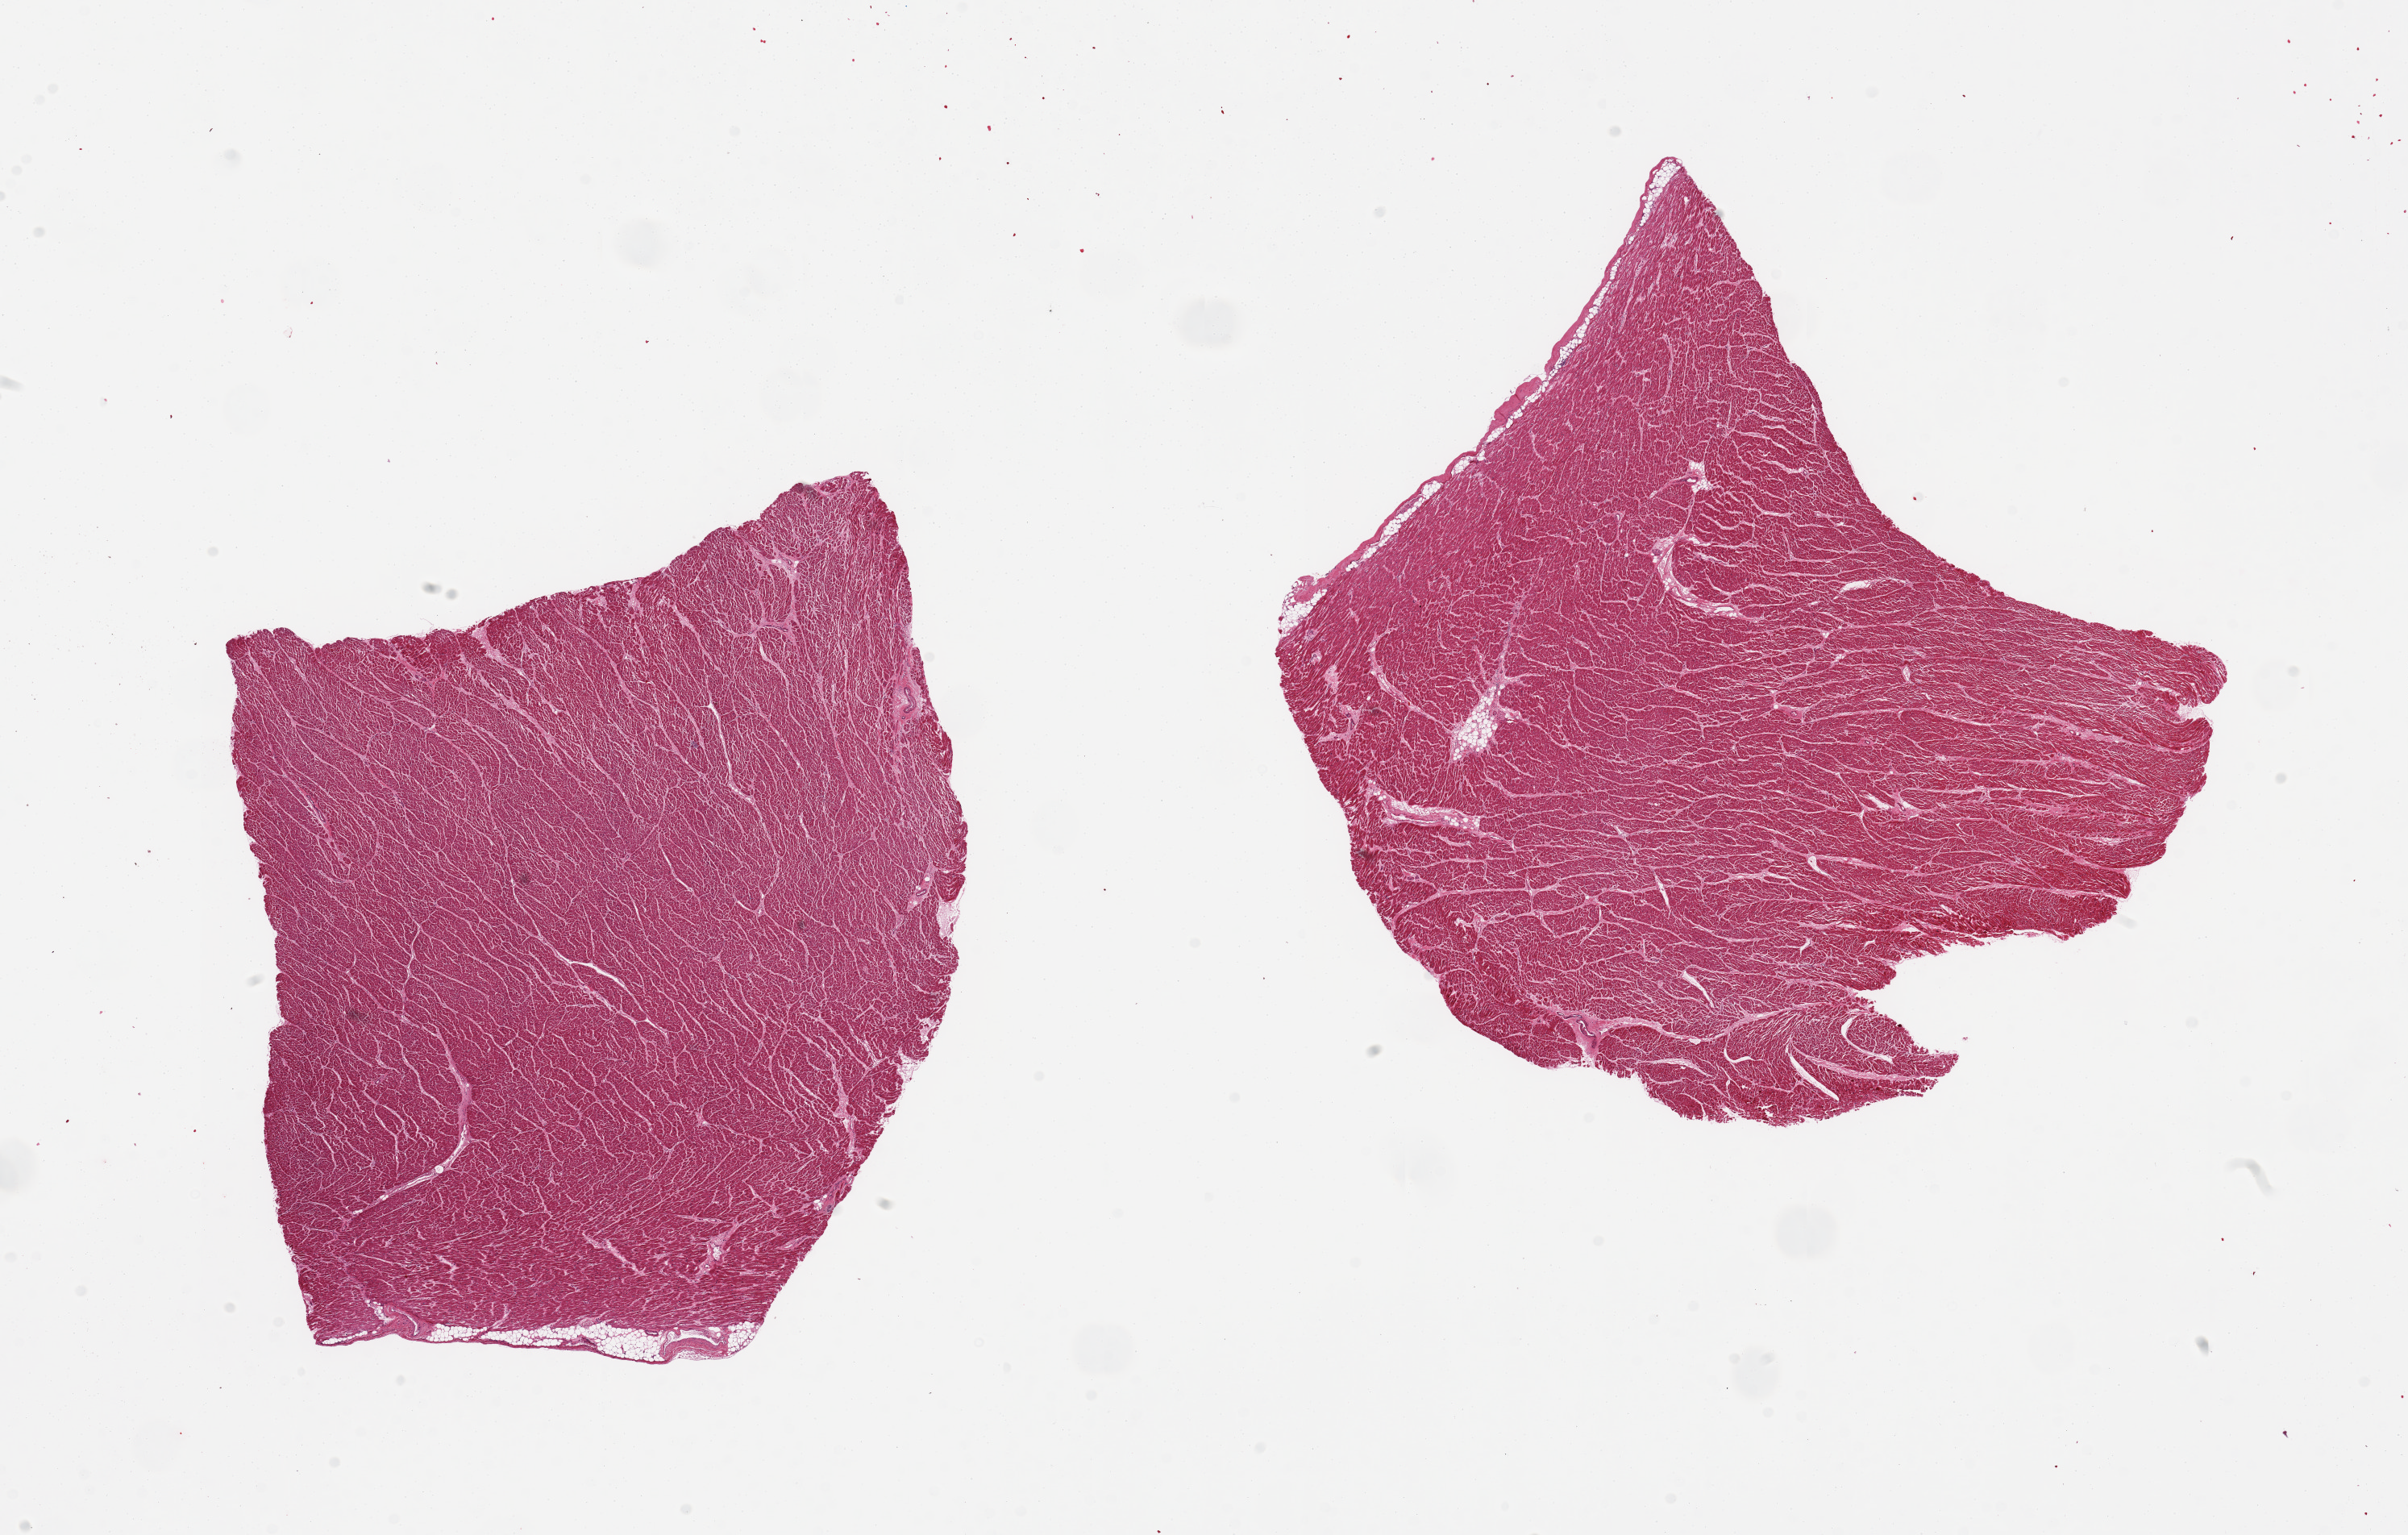
Digitized haematoxylin and eosin-stained section, whole scanned area (about 23.6 x 15.1 mm, slide scanned at 20x) shown as a low-resolution overview. PAXgene-fixed, paraffin-embedded tissue. Sampled site (target tissue): heart. Tissue donor sample.
Reviewer comment on this tissue sample: 2 pieces.